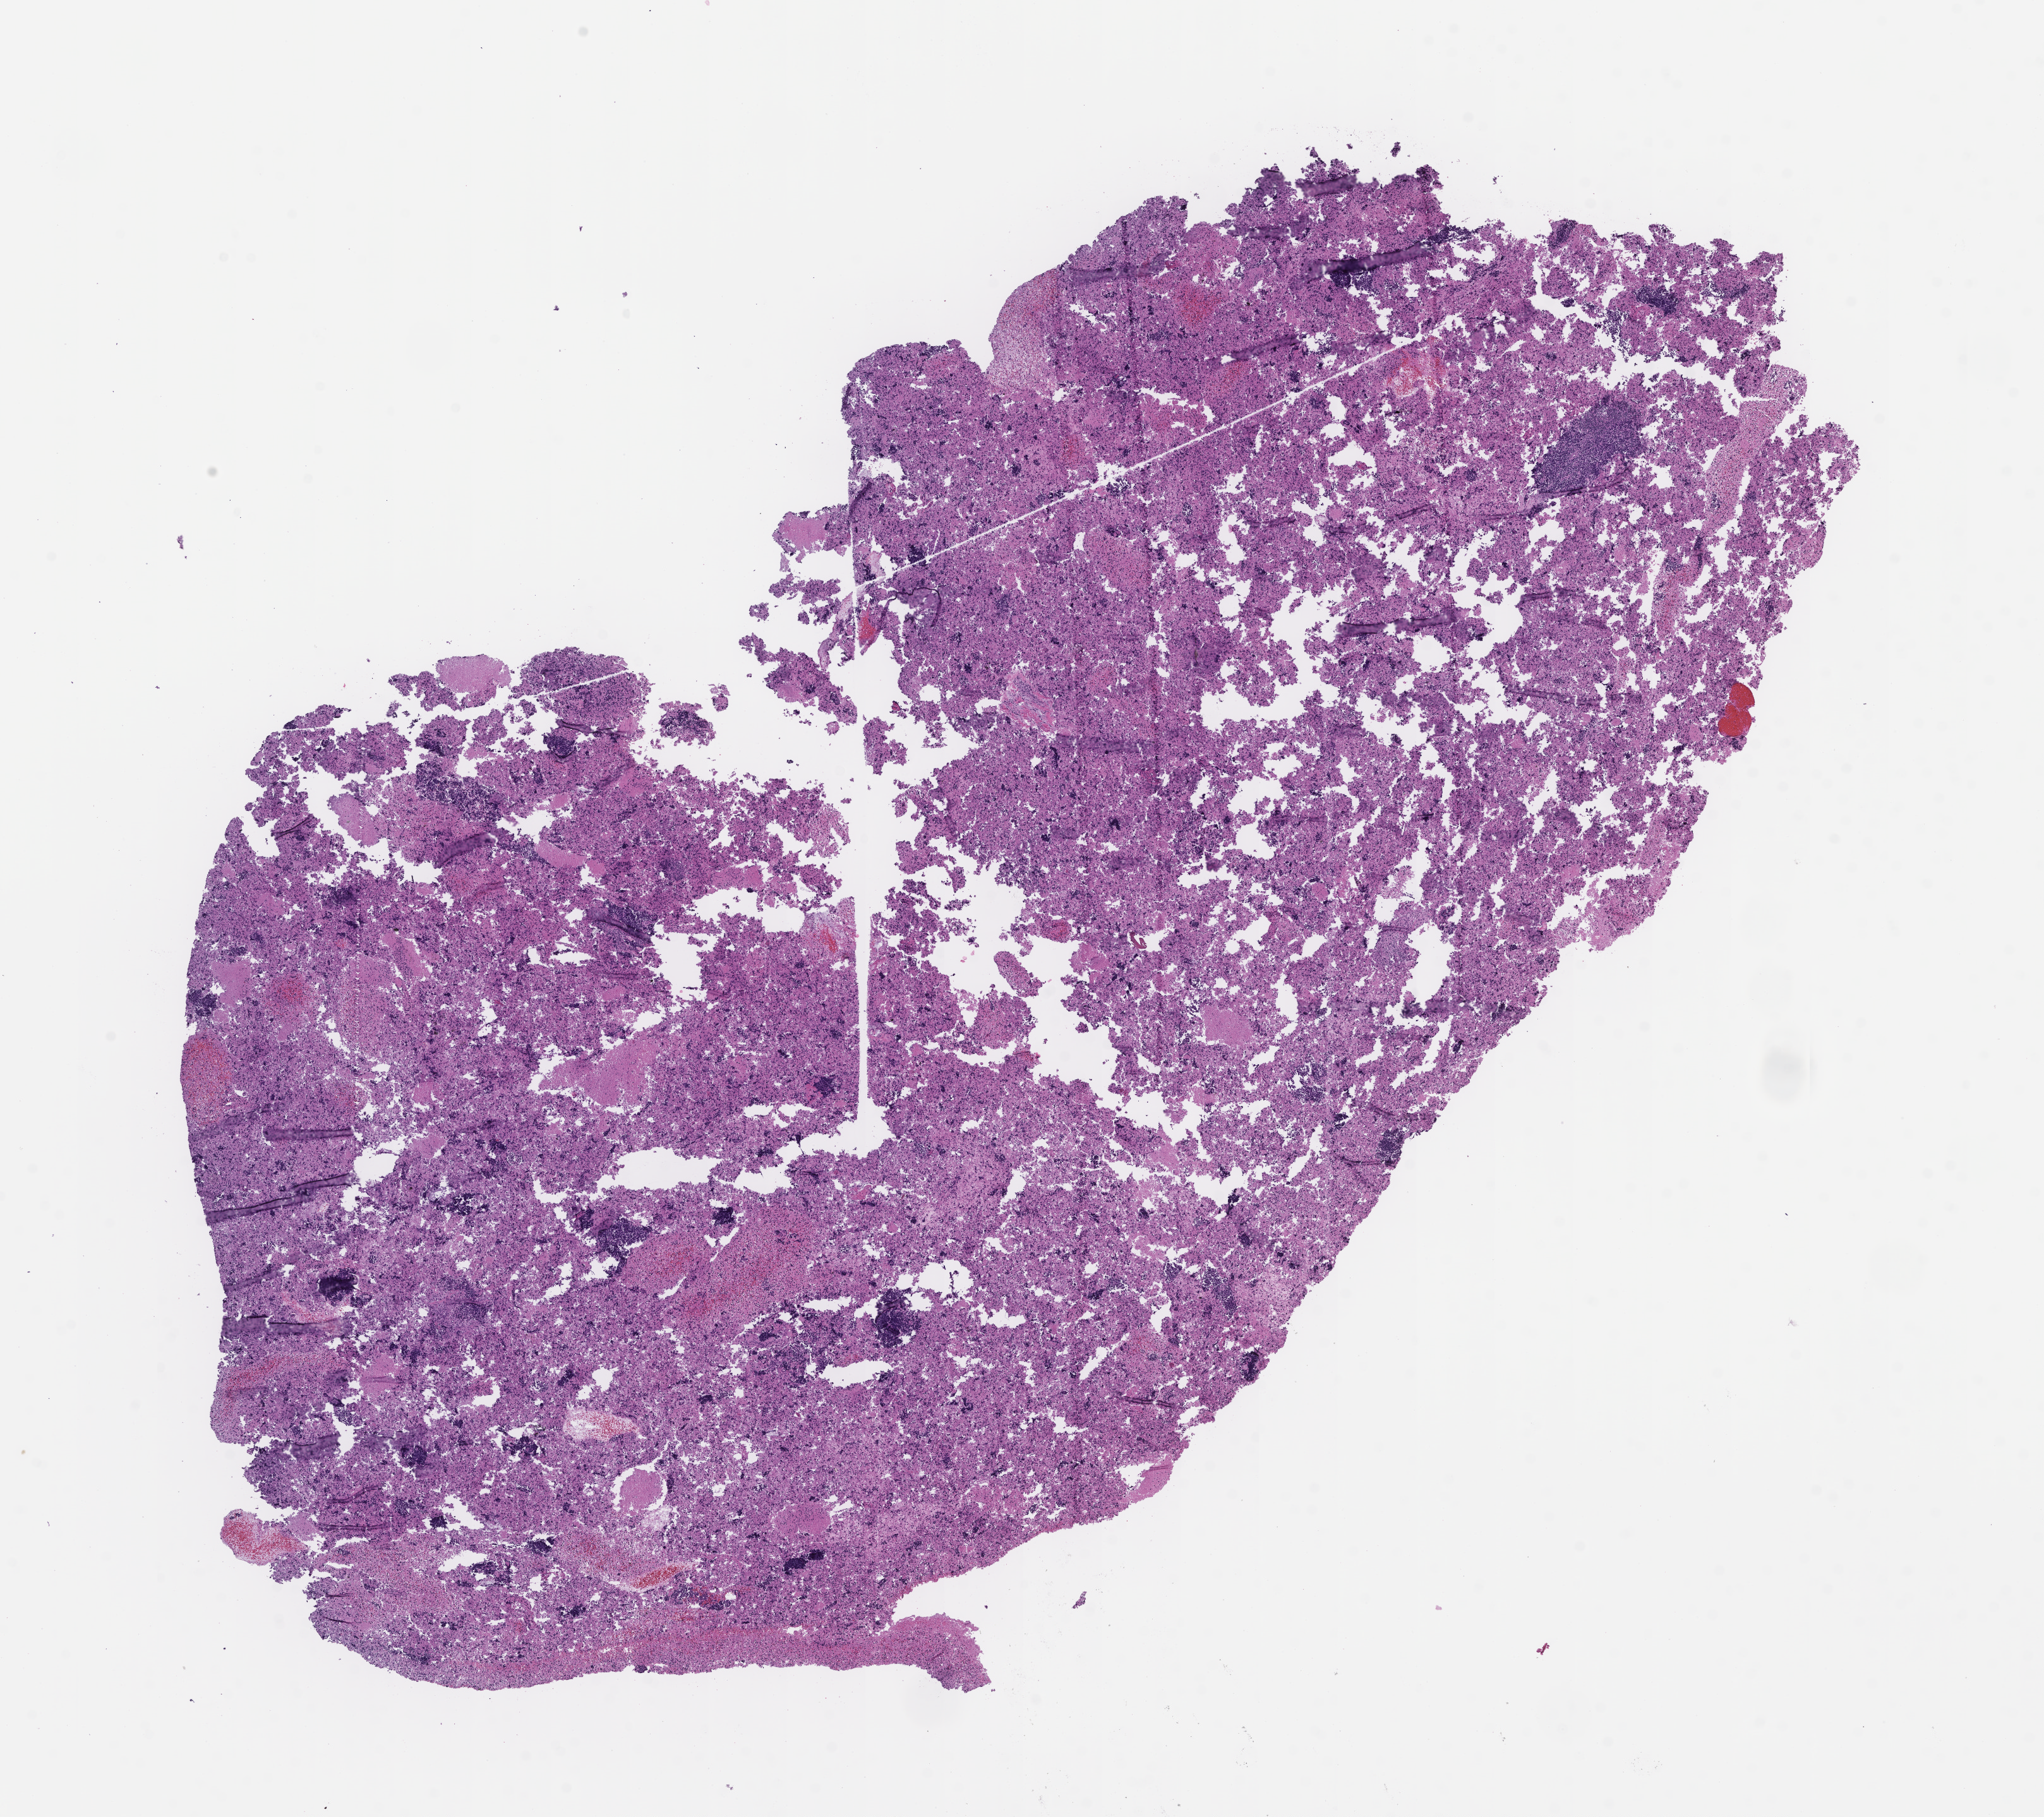
Whole-slide image, hematoxylin and eosin (H&E) stain, a low-resolution overview of the entire scanned area, about 13.1 x 11.6 mm, formalin-fixed, paraffin-embedded (FFPE) tissue, site: lung, archival tissue. Patient sex: female.
* this section: primary tumor
* diagnosis: Small Cell Lung Carcinoma